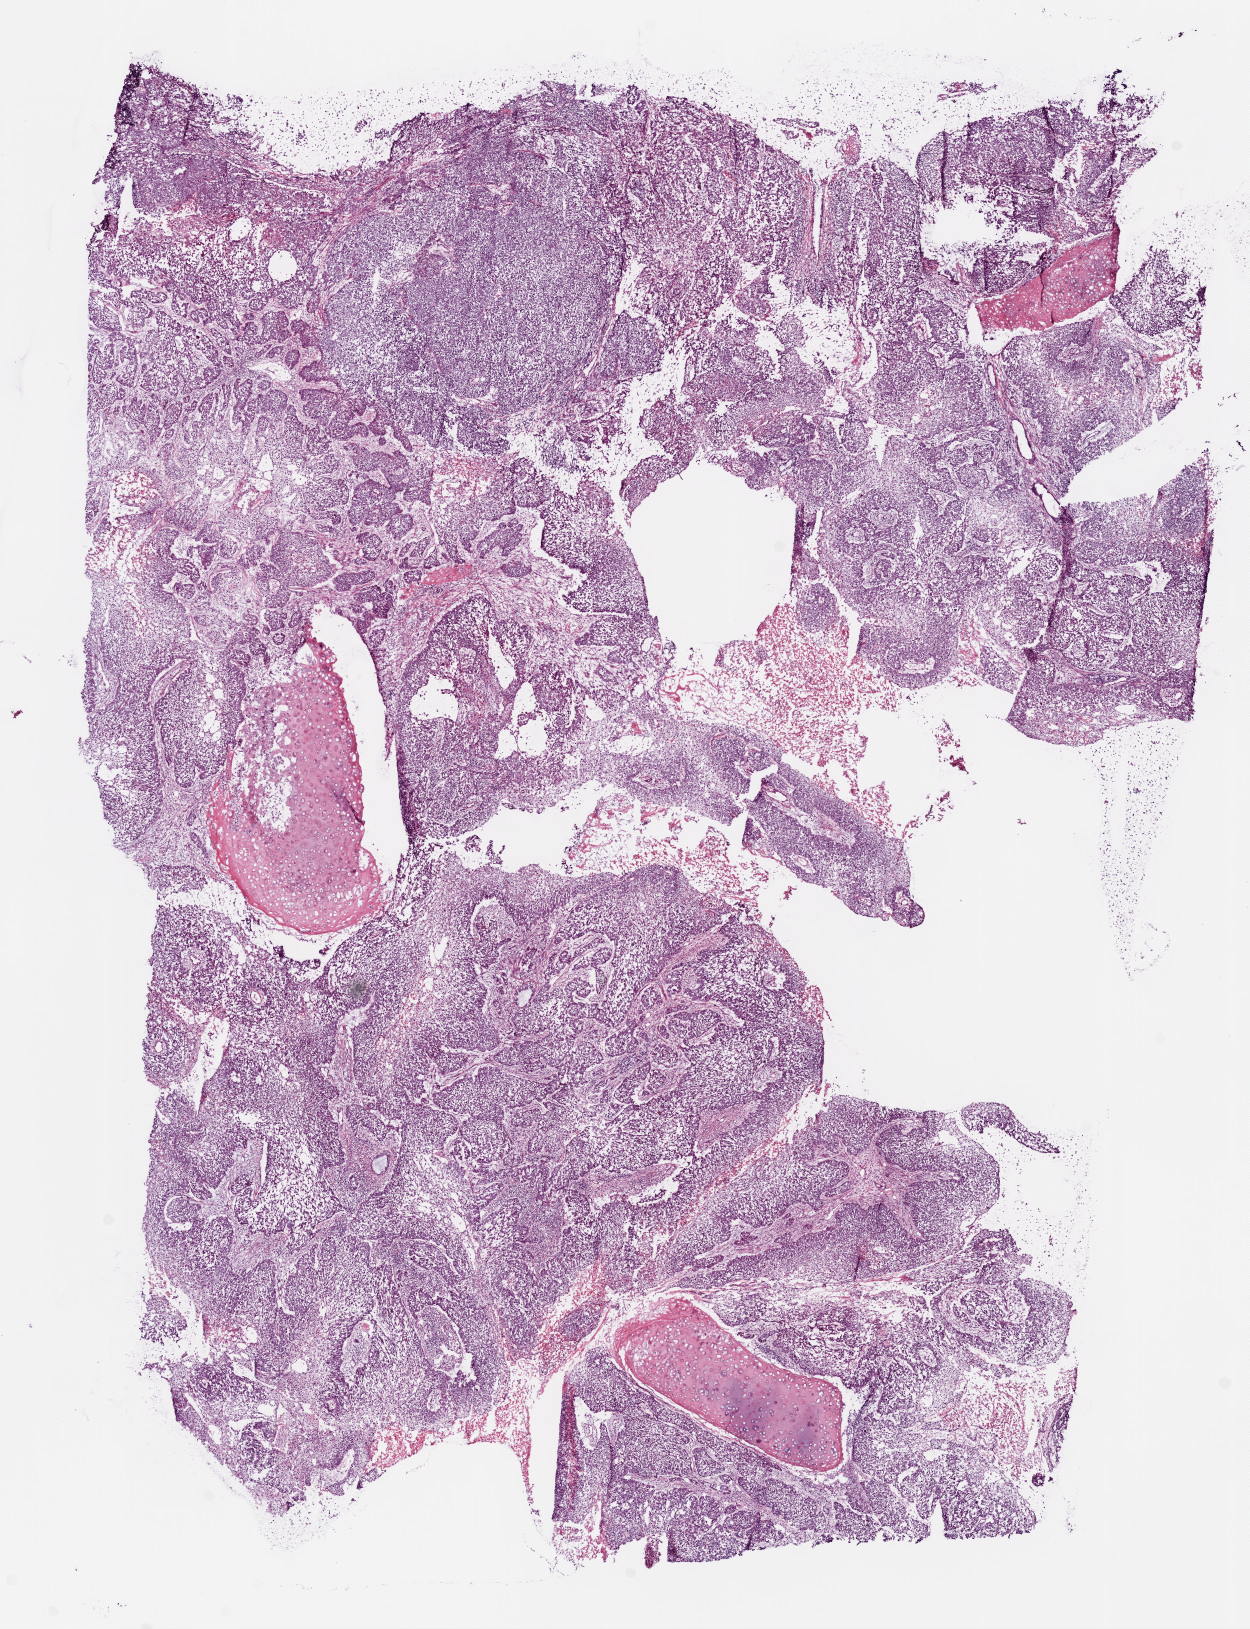
Digitized Hematoxylin and eosin (H&E) stained tissue section (whole slide), shown as a low-resolution overview of the whole scanned area (about 10.0 x 13.1 mm, from a 20x scan). Frozen section from the bottom of the tissue portion. Primary tumour sample from the lung. Male patient; age at initial diagnosis 72 years. Slide review estimates, as recorded: tumour cells 80%, tumour nuclei 75%, normal cells 0%, stromal cells 15%, necrosis 5%.
AJCC pathologic stage: IA. Pathologic diagnosis: Squamous cell carcinoma, NOS.